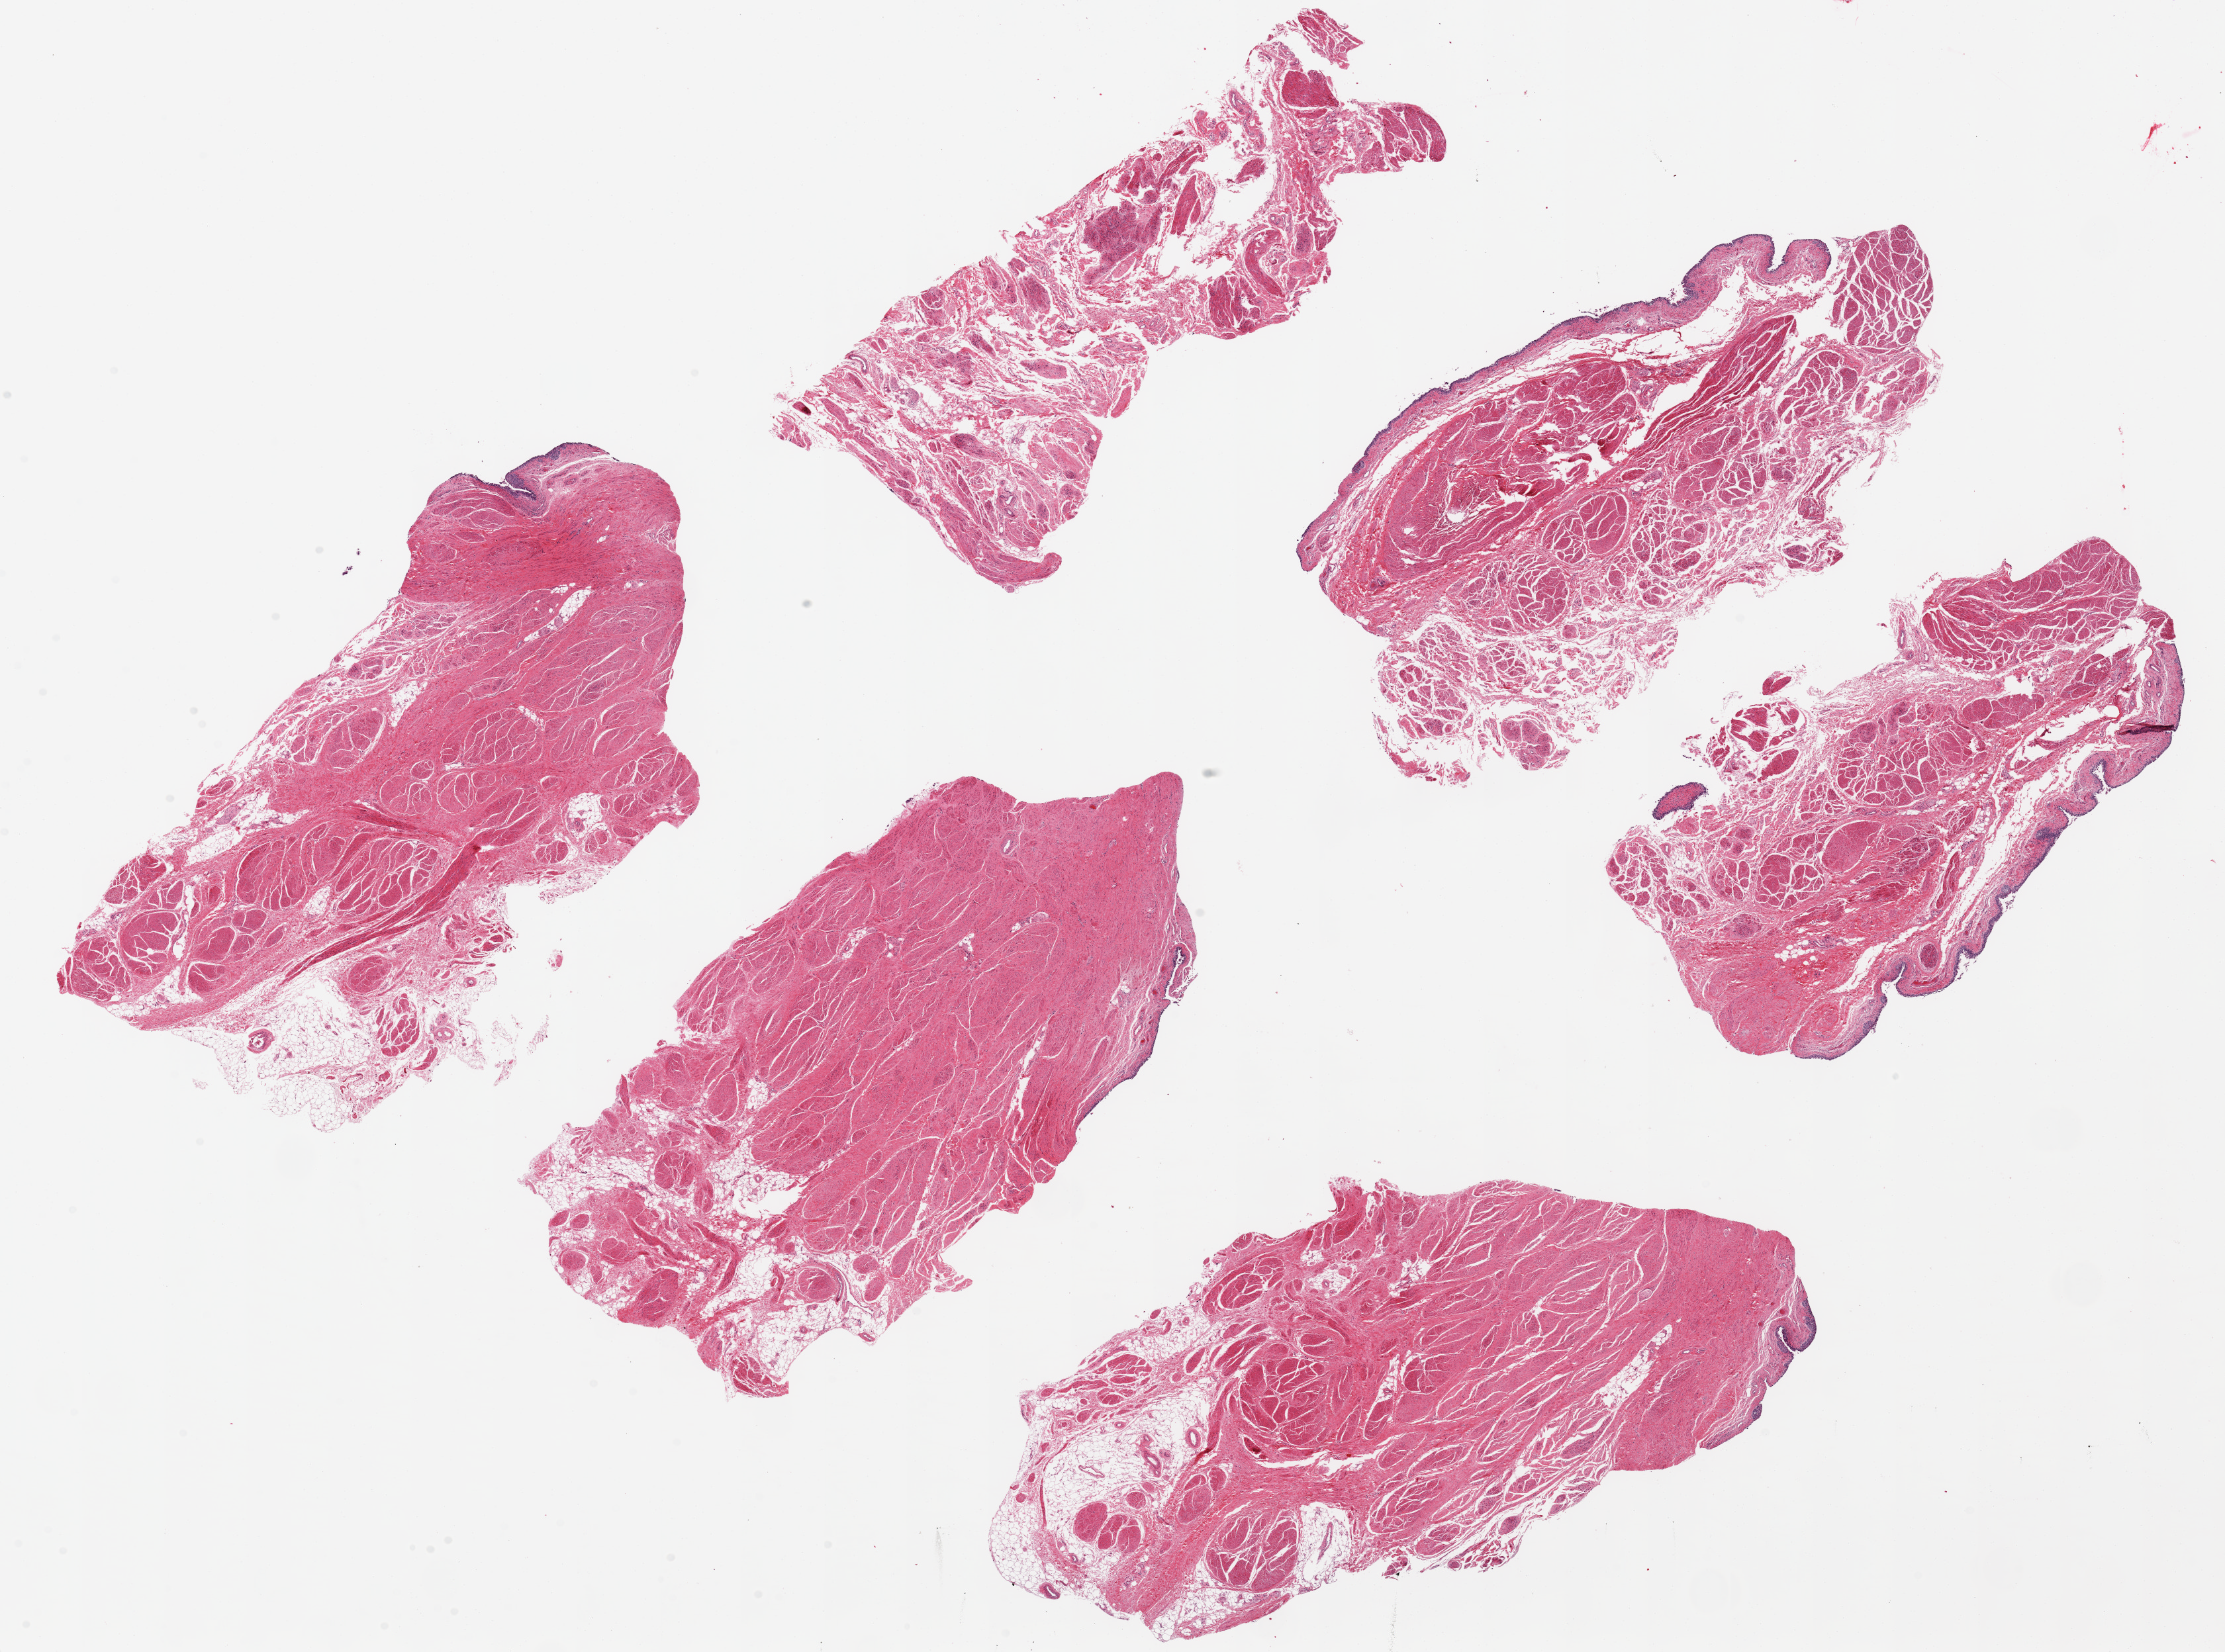
Whole-slide image, haematoxylin and eosin stain — shown as a low-resolution overview of the whole scanned area (about 26.6 x 19.7 mm), PAXgene-fixed paraffin-embedded (PFPE) section, target tissue: urinary bladder, donor tissue sample. Donor sex: male.
Pathologist's review note for this sample: 6 ~8.5x4mm pieces. Urothelium is <1% of thickness, partly sloughed; some areas of cystitis cystica/ reactive changes.